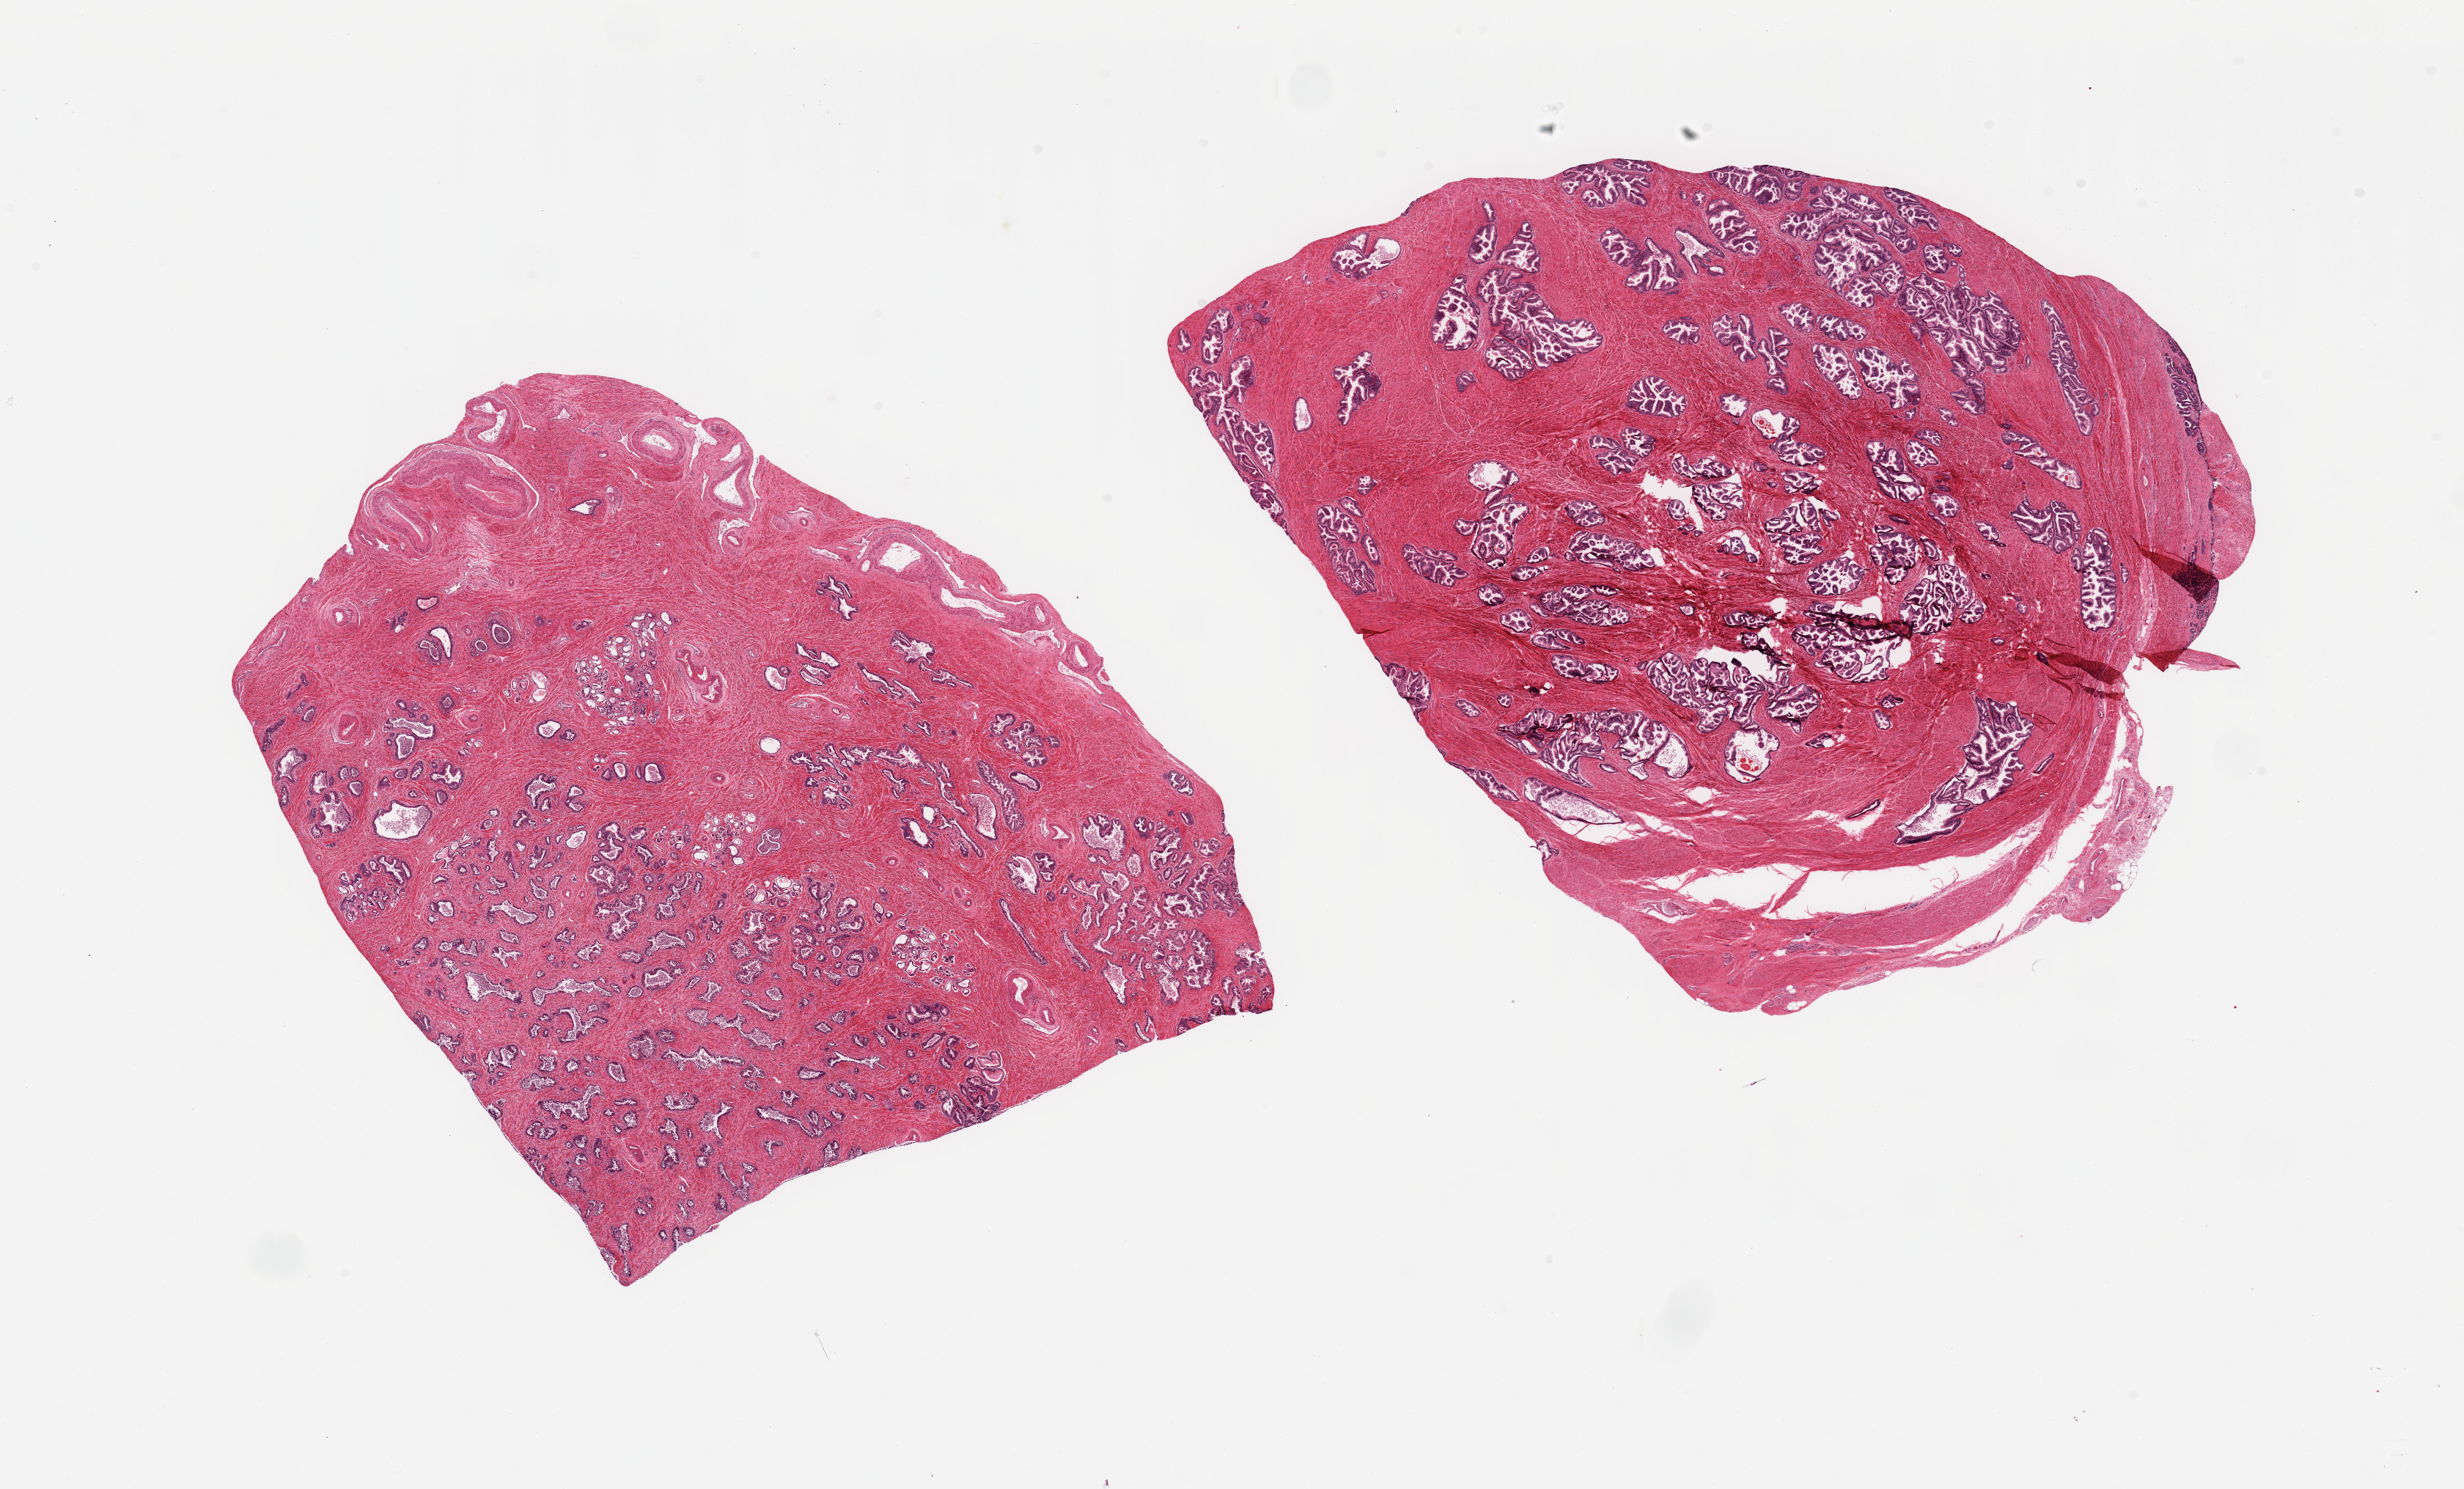
Whole-slide image, H&E stain, whole scanned area (about 26.6 x 16.1 mm, slide scanned at 20x) shown as a low-resolution overview. PAXgene-fixed, paraffin-embedded tissue. Target tissue: prostate. Donor tissue sample. Donor: male.
Reviewer comment on this tissue sample: 2 pieces, hyperplastic glandular pattern.